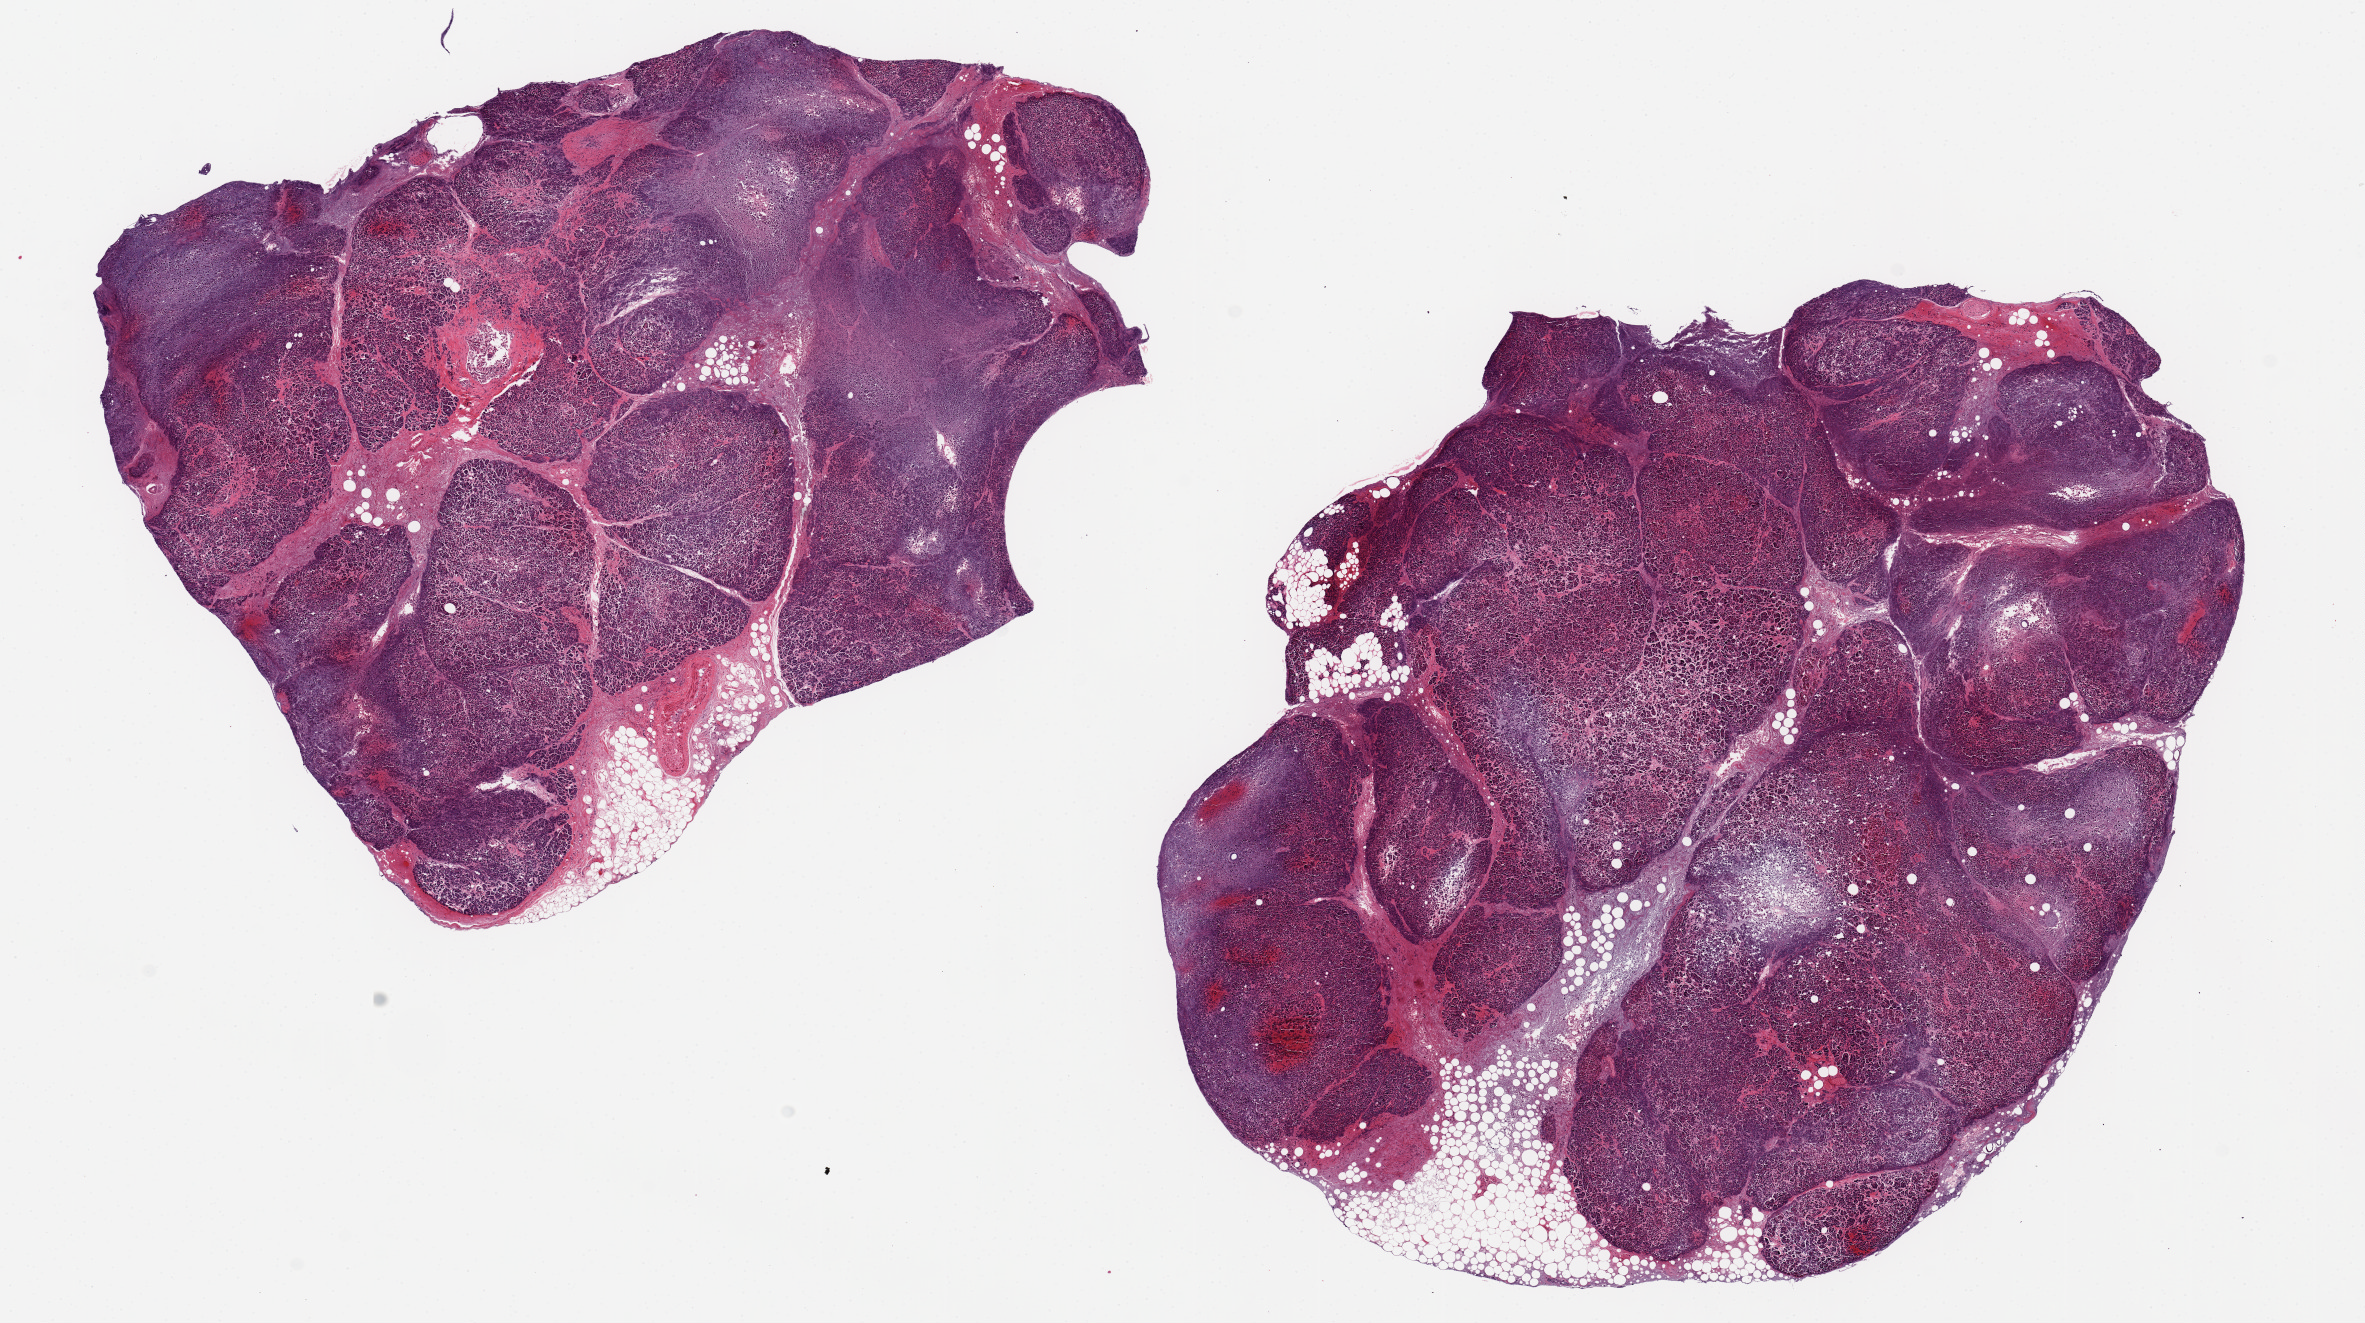
Whole-slide image, haematoxylin and eosin stain, a low-resolution overview of the entire scanned area, about 18.7 x 10.5 mm (from a 20x scan). PAXgene-fixed paraffin-embedded (PFPE) section. Target tissue: pancreas. Tissue donor sample.
- reviewer comment on this tissue sample: 2 ~7.5x7mm aliquots. Severe post mortem saponification; about 10% peripheral and interstital adipose tissue